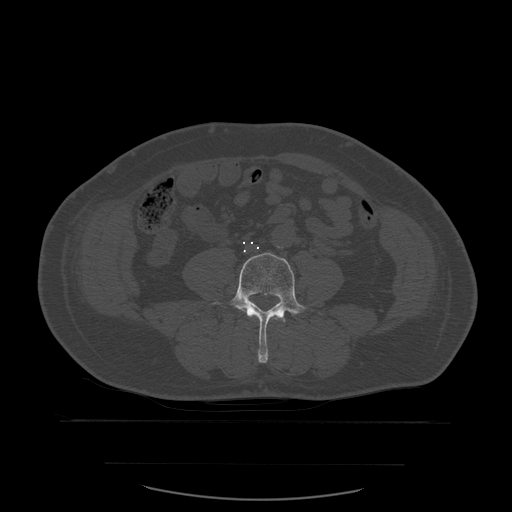
CT including the spine, one axial slice. Position 166 of 590 along the scan axis. Bone window (W 1800 / L 400 HU). 512 × 512 image matrix, field of view 479 × 479 mm. Patient age 71 years. From the clinical record (not read from this slice): primary cancer: lung.
Structures marked on this image (semi-automatically segmented with operator editing):
- L3 vertebra: box from (x=272, y=315) to (x=281, y=320) px
- L4 vertebra: (x=210, y=253)–(x=307, y=363)